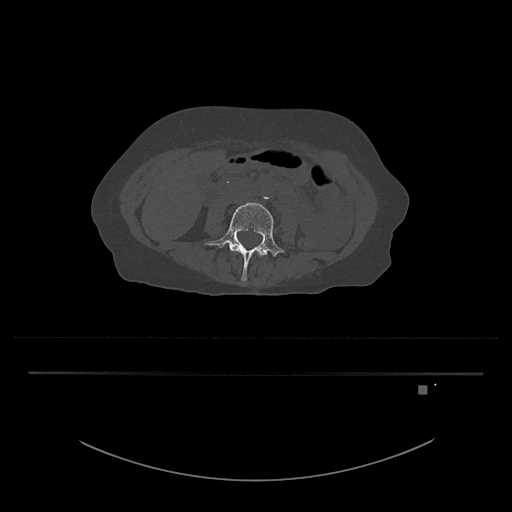
CT including the spine, one axial slice; bone window (W 1800 / L 400 HU); 512 × 512 image matrix. Patient: female, 57 years. Case-level facts recorded for this patient, not image findings: primary cancer: cervical.
Structures marked on this image (semi-automatic segmentation, software-assisted and operator-edited):
- L3 vertebra: bounding box (x1, y1, x2, y2) in pixels: (258, 252, 262, 257)
- L4 vertebra: (204, 202, 285, 281)